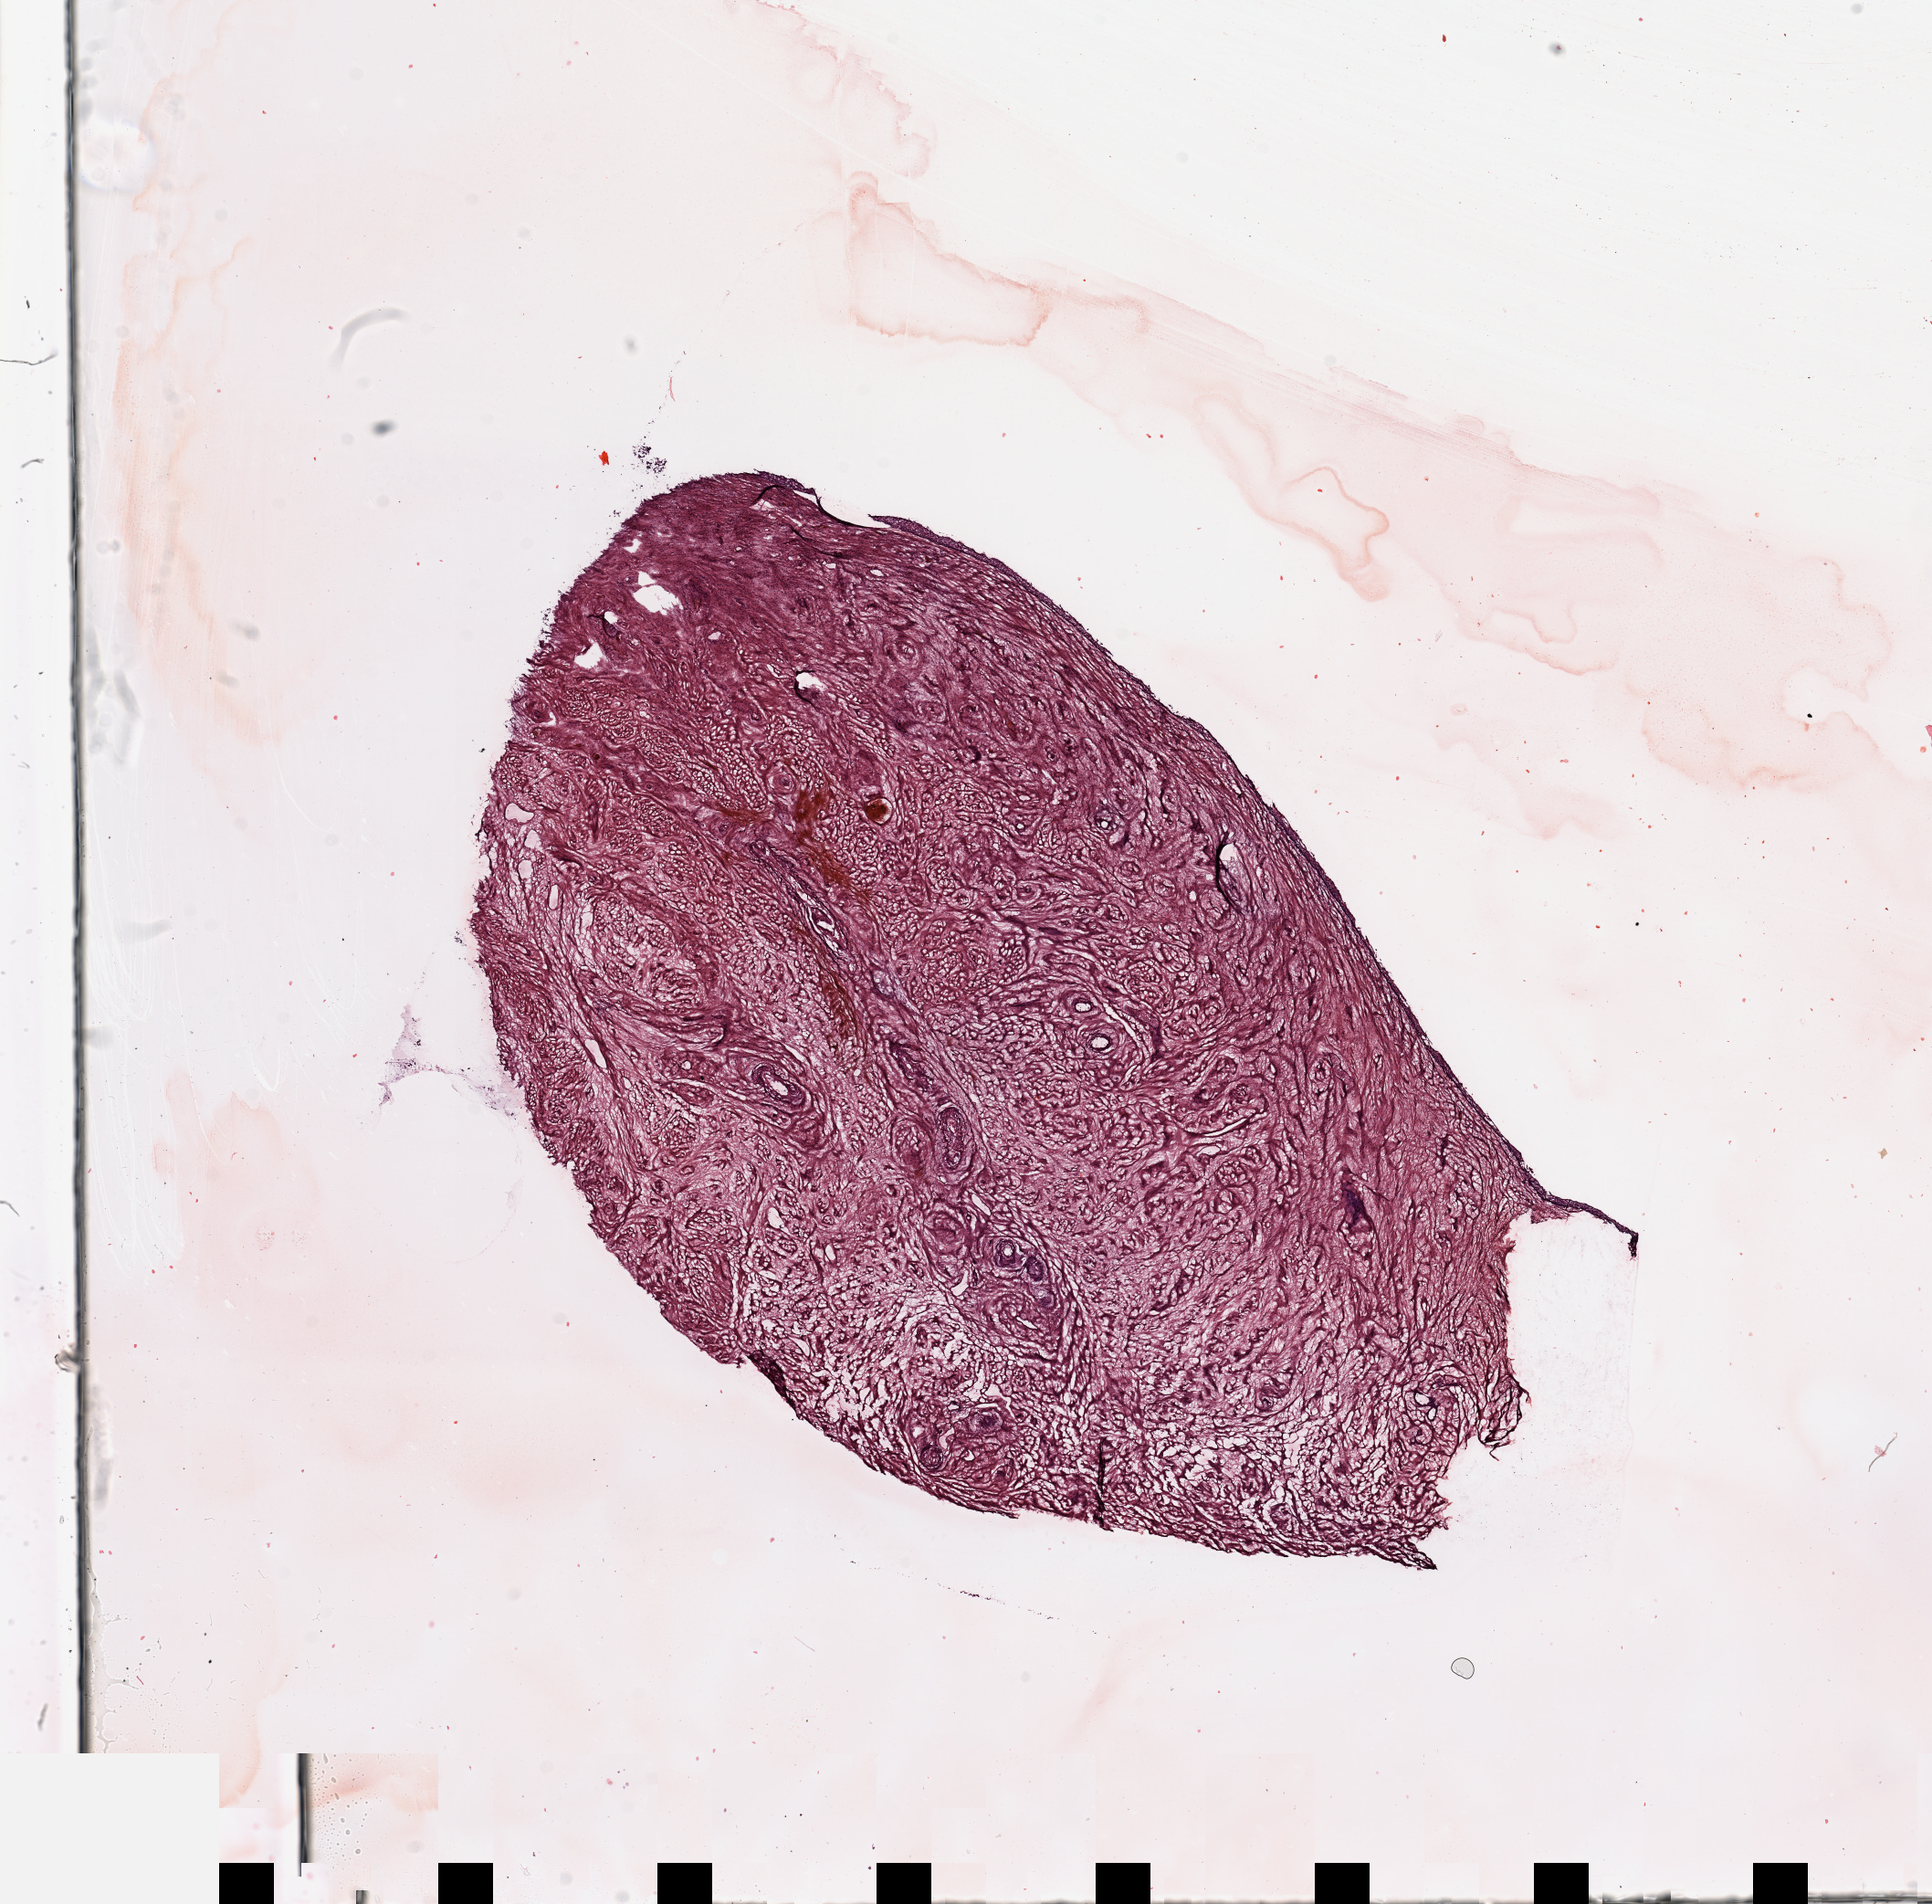
H&E whole-slide image — a low-resolution overview of the entire scanned area, about 16.7 x 16.5 mm. Normal (non-tumour) tissue sample, uterus. Patient: female, age 75 years.
This section: normal (non-tumour) tissue from the same patient. Patient diagnosis: Endometrioid adenocarcinoma, NOS.